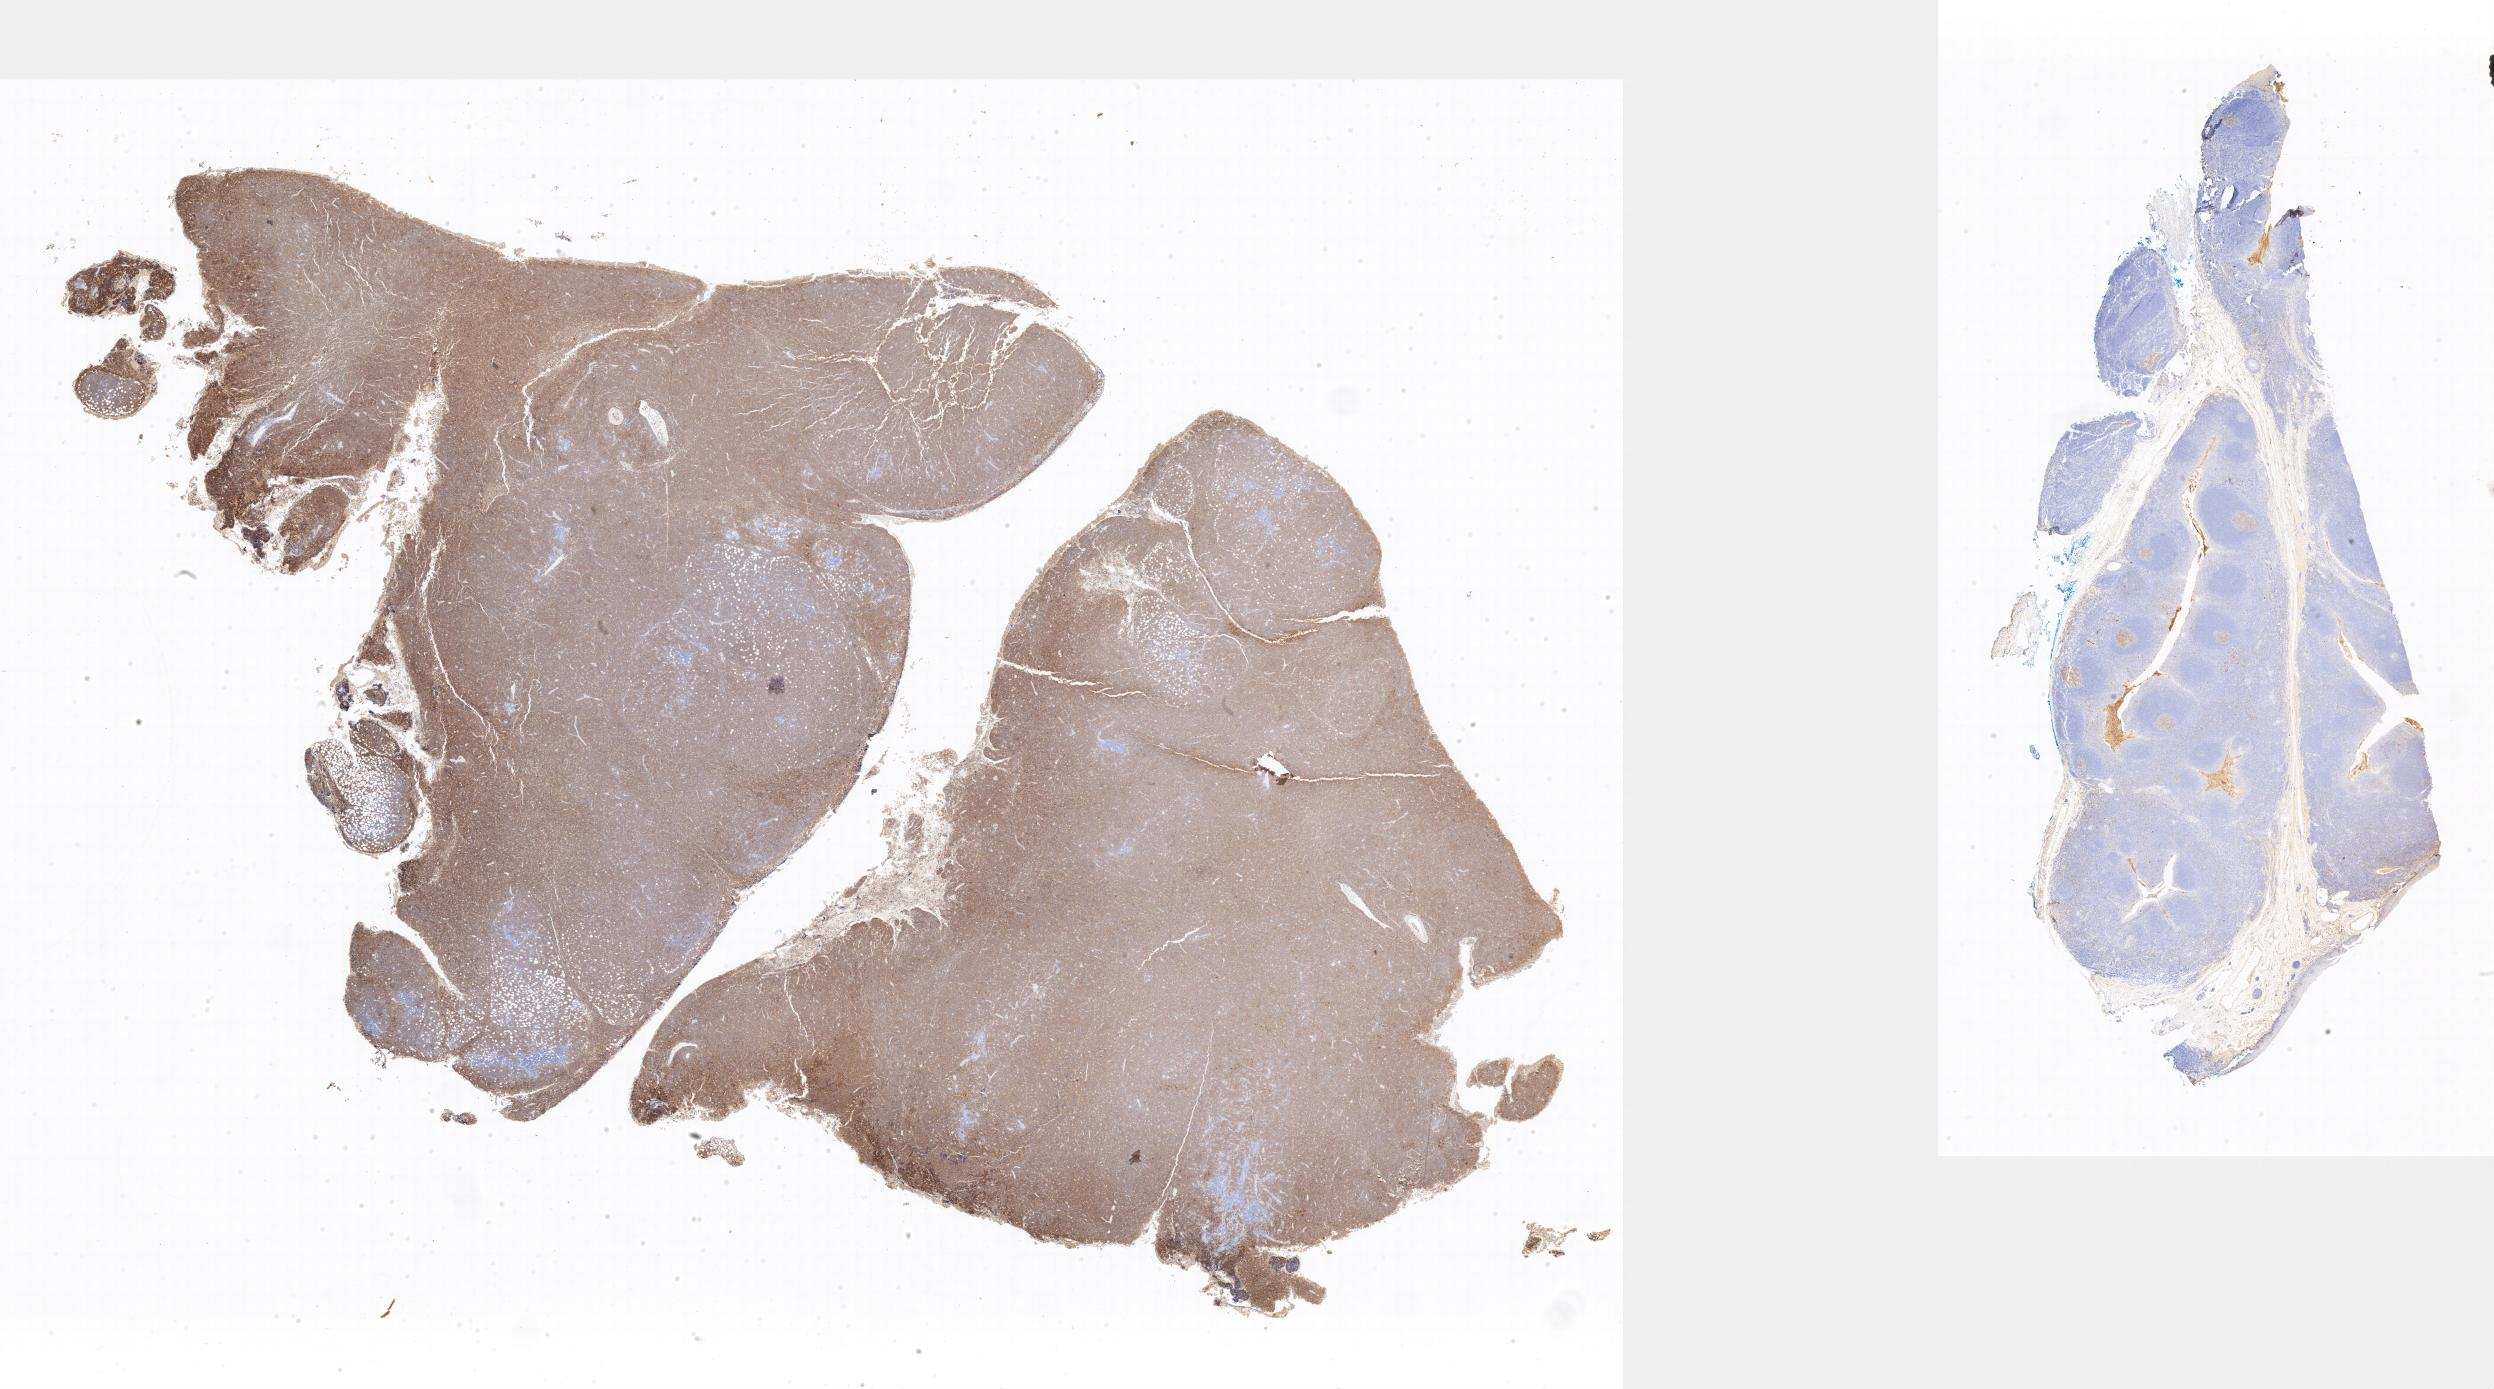
Whole-slide image, immunohistochemical stain for CD10 — shown as a low-resolution overview of the whole scanned area. Tumor tissue. Anatomic site: peritoneum. Male, age 9 years at initial diagnosis.
Diagnosis: Burkitt lymphoma, NOS.